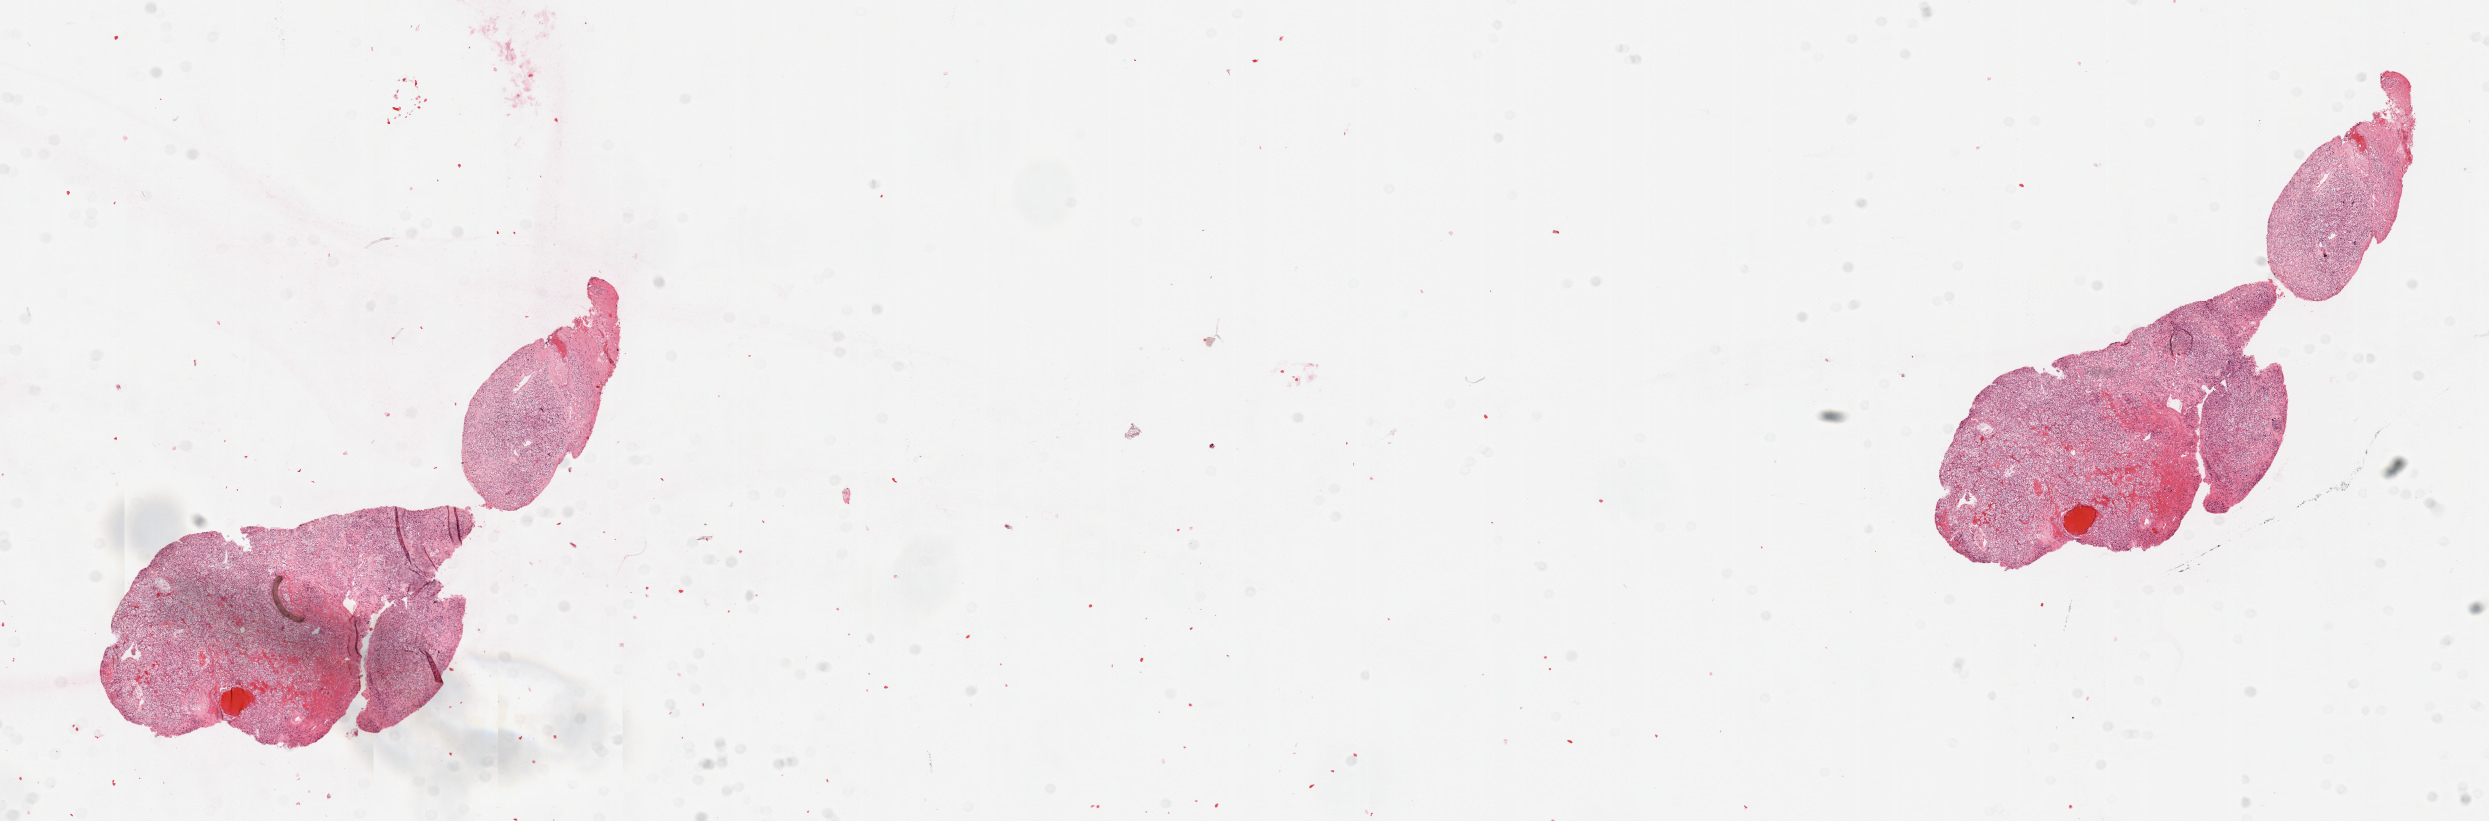
Digitized Hematoxylin and eosin (H&E) stained tissue section (whole slide) — low-resolution overview of the scanned area, about 19.7 x 6.5 mm (acquisition: 20x scan); tumour tissue sample, sampled site: kidney. 46-year-old male patient. Histologic grade: G2 (moderately differentiated). Composition of this section per pathologist review: tumour nuclei 90%, necrosis 5%.
AJCC pathologic stage: I. Diagnosis: Renal cell carcinoma, NOS.